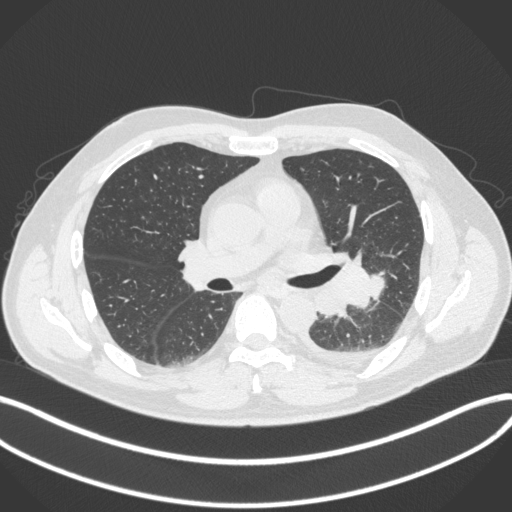
Chest CT, one axial slice; slice 204 of 350 in the series (ordered by position); lung window (W 1500 / L -600 HU); 1 mm slice thickness; 512 × 512 image matrix, field of view 400 × 400 mm. Patient: male, 58 years. From the clinical record (not read from this slice): clinical TNM (as recorded): T3 N1 M1b.
Structures marked on this image (bounding box drawn by a radiologist):
- lung tumour (recorded histology: small cell carcinoma): bounding box [x1, y1, x2, y2] px = [313, 253, 389, 317]